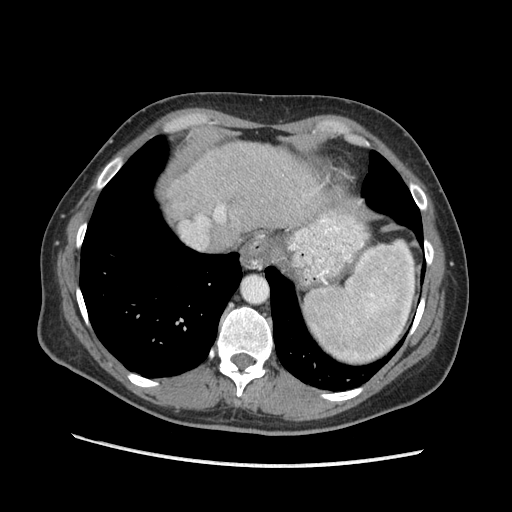
Contrast-enhanced abdominal CT (liver protocol), one axial slice; position 153 of 170 along the scan axis; reconstruction kernel STANDARD; soft-tissue window (W 400 / L 40 HU); 2.5 mm slice thickness; 512 × 512 image matrix. From the clinical record (not read from this slice): diagnosis: hepatocellular carcinoma (patient treated with transarterial chemoembolisation; whether this scan precedes or follows treatment is not stated here); TNM stage (as recorded): Stage-II; Child-Pugh class: A; tumour nodularity: multinodular.
Structures marked on this image (semi-automatic segmentation, software-assisted and operator-edited):
- abdominal aorta: bounding box (x1, y1, x2, y2) in pixels: (242, 276, 267, 302)
- liver parenchyma outside the tumour (the mass and vessels are separate outlines, so this box may not span the whole liver): (164, 142, 326, 232)
- liver vessels: (197, 206, 225, 224)